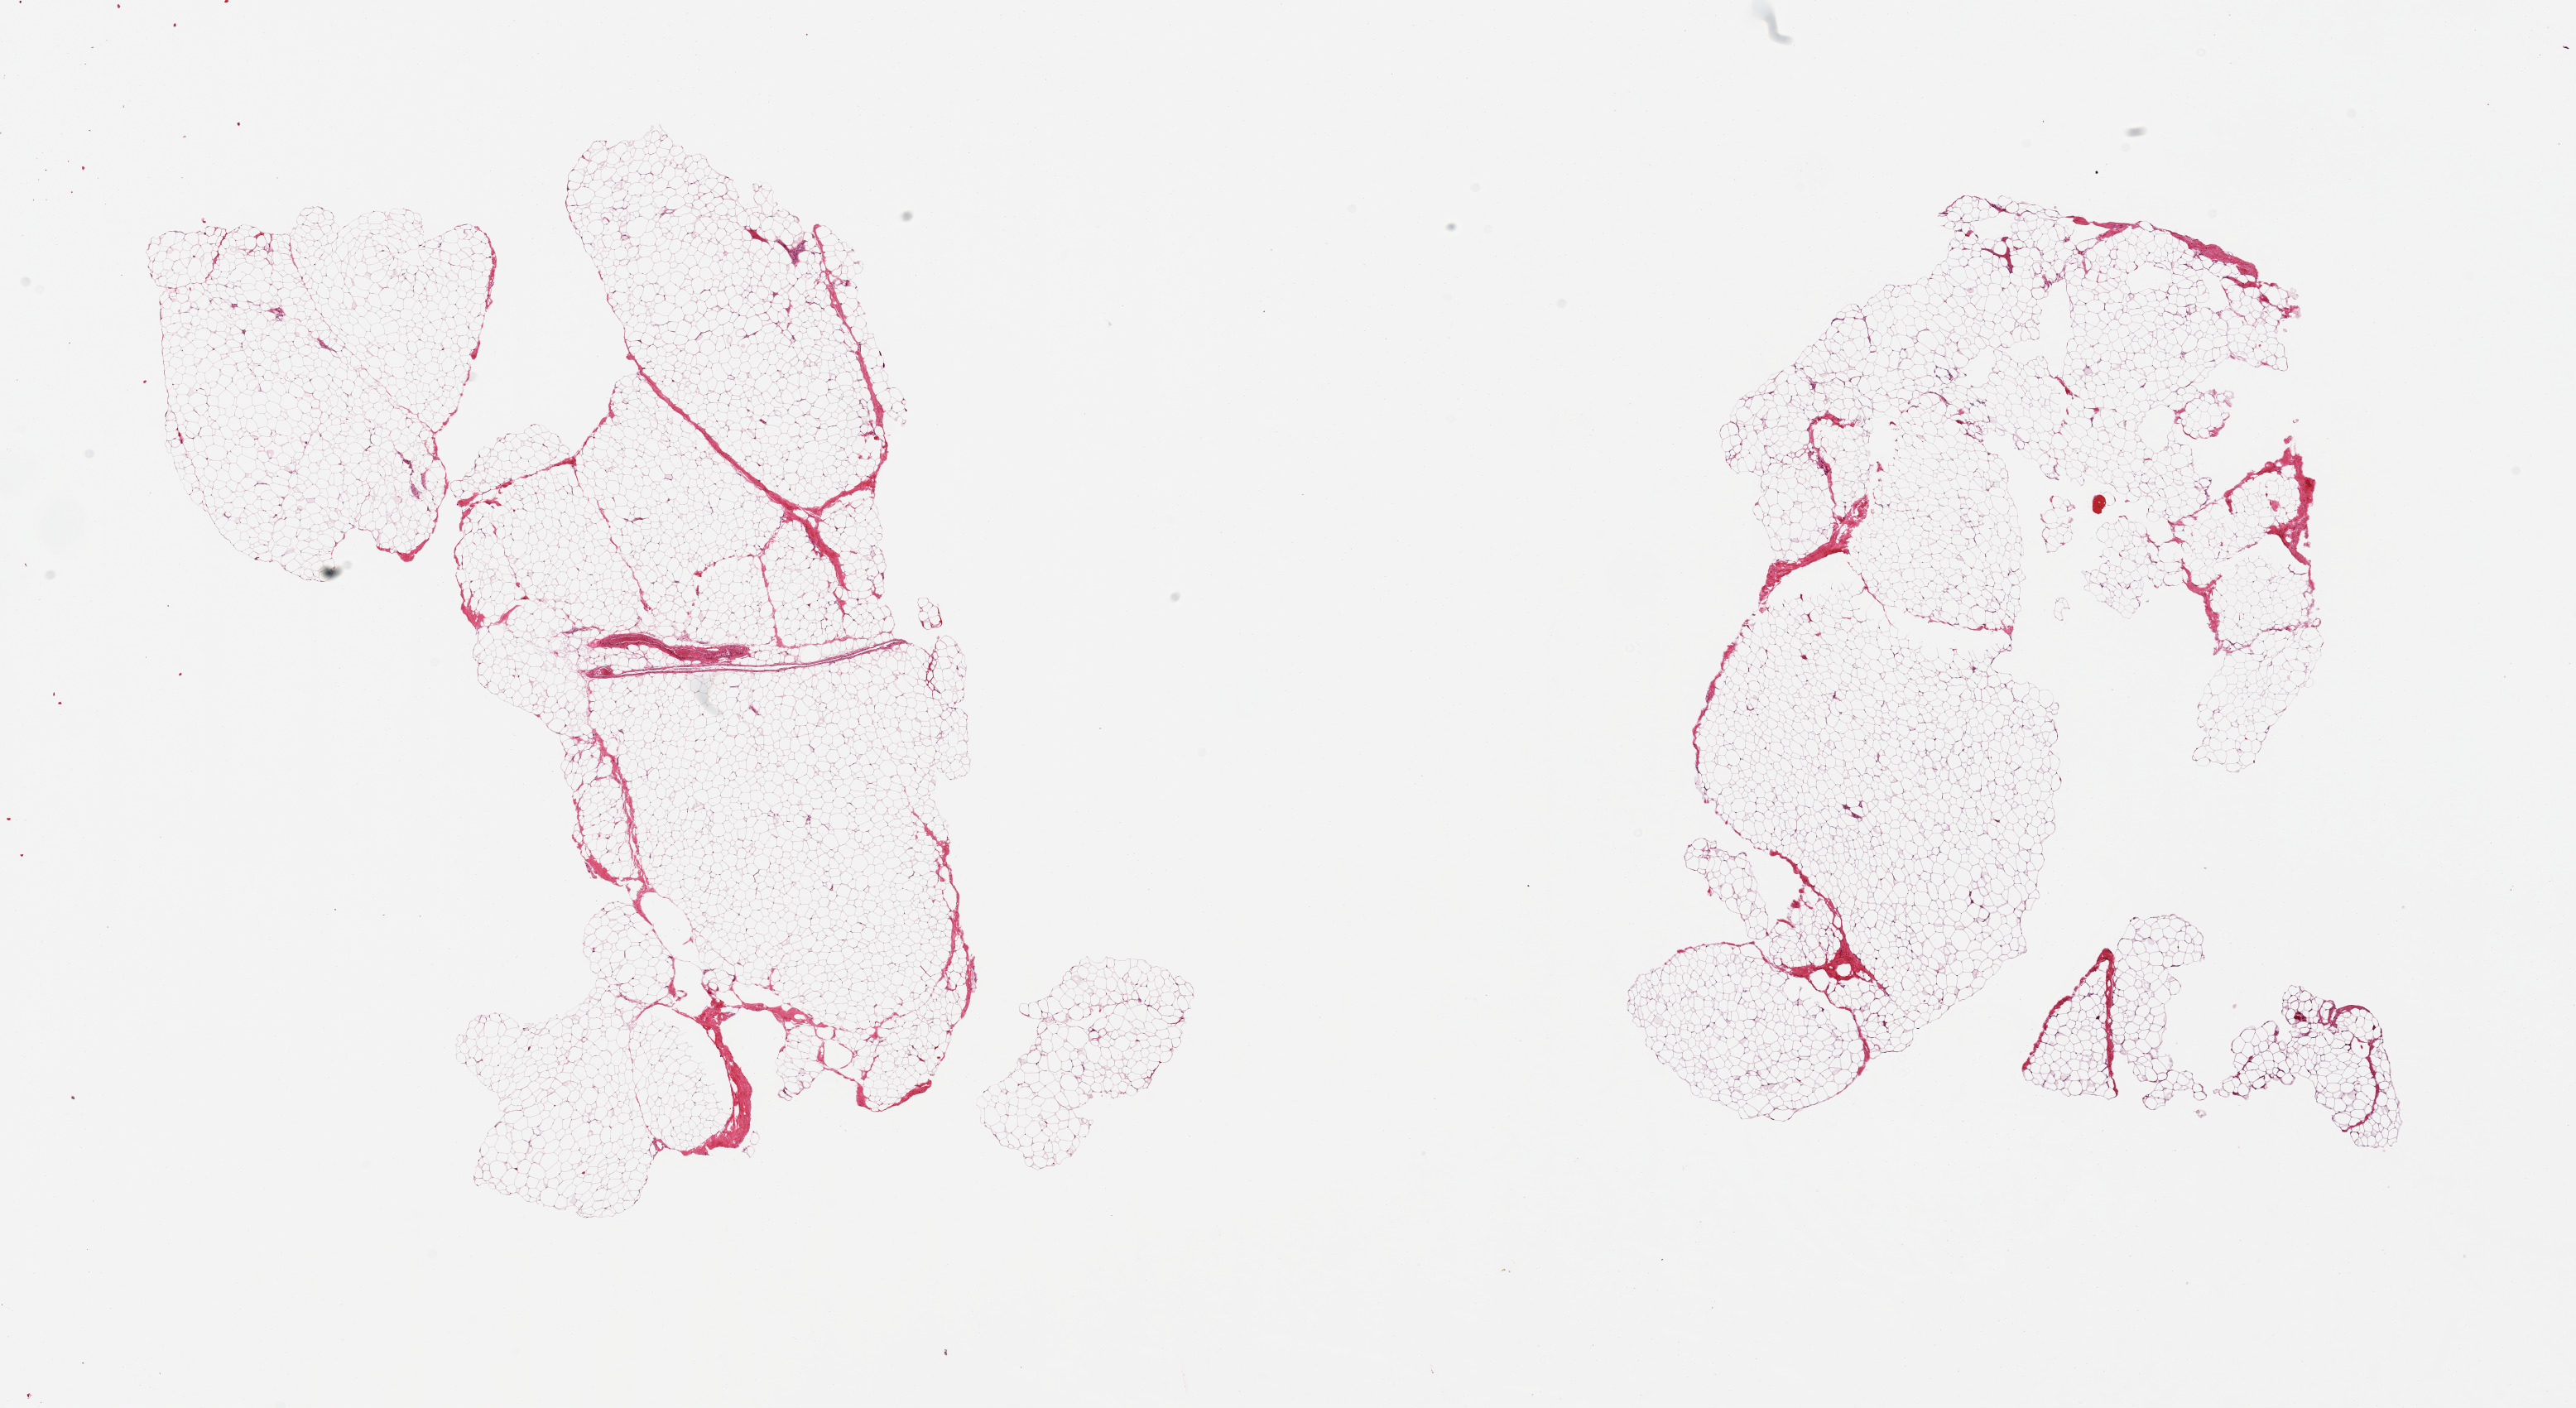
Digitized hematoxylin and eosin (H&E)-stained section — low-resolution overview of the scanned area, about 24.6 x 13.5 mm. PAXgene-fixed, paraffin-embedded tissue. Target tissue: breast. Donor tissue sample. Male donor.
Pathologist's review note for this sample: 2 pieces, fibroadipose elements only.